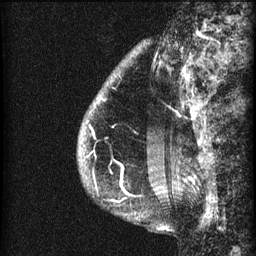
Breast MRI (dynamic contrast-enhanced), one sagittal slice. Slice 11 of 60 in the series (ordered by position). 3 images stored at this slice position (order not interpretable as contrast timing). 1.5 T. TE 4.2 ms, TR 22.7 ms. 2 mm slice thickness. 256 × 256 image matrix. Patient: female, 48 years. Case-level facts recorded for this patient, not image findings: setting: breast cancer imaged before/during neoadjuvant chemotherapy; receptor status: triple-negative.
Outlined on this slice (semi-automatic segmentation, software-assisted and operator-edited):
- analysis volume of interest (the breast-tissue region the enhancement analysis was run in; not a lesion): box from (x=79, y=30) to (x=173, y=207) px
- tumour enhancement mask (voxels above the 90 % enhancement threshold inside the analysis volume of interest): (x=104, y=98)–(x=107, y=100)